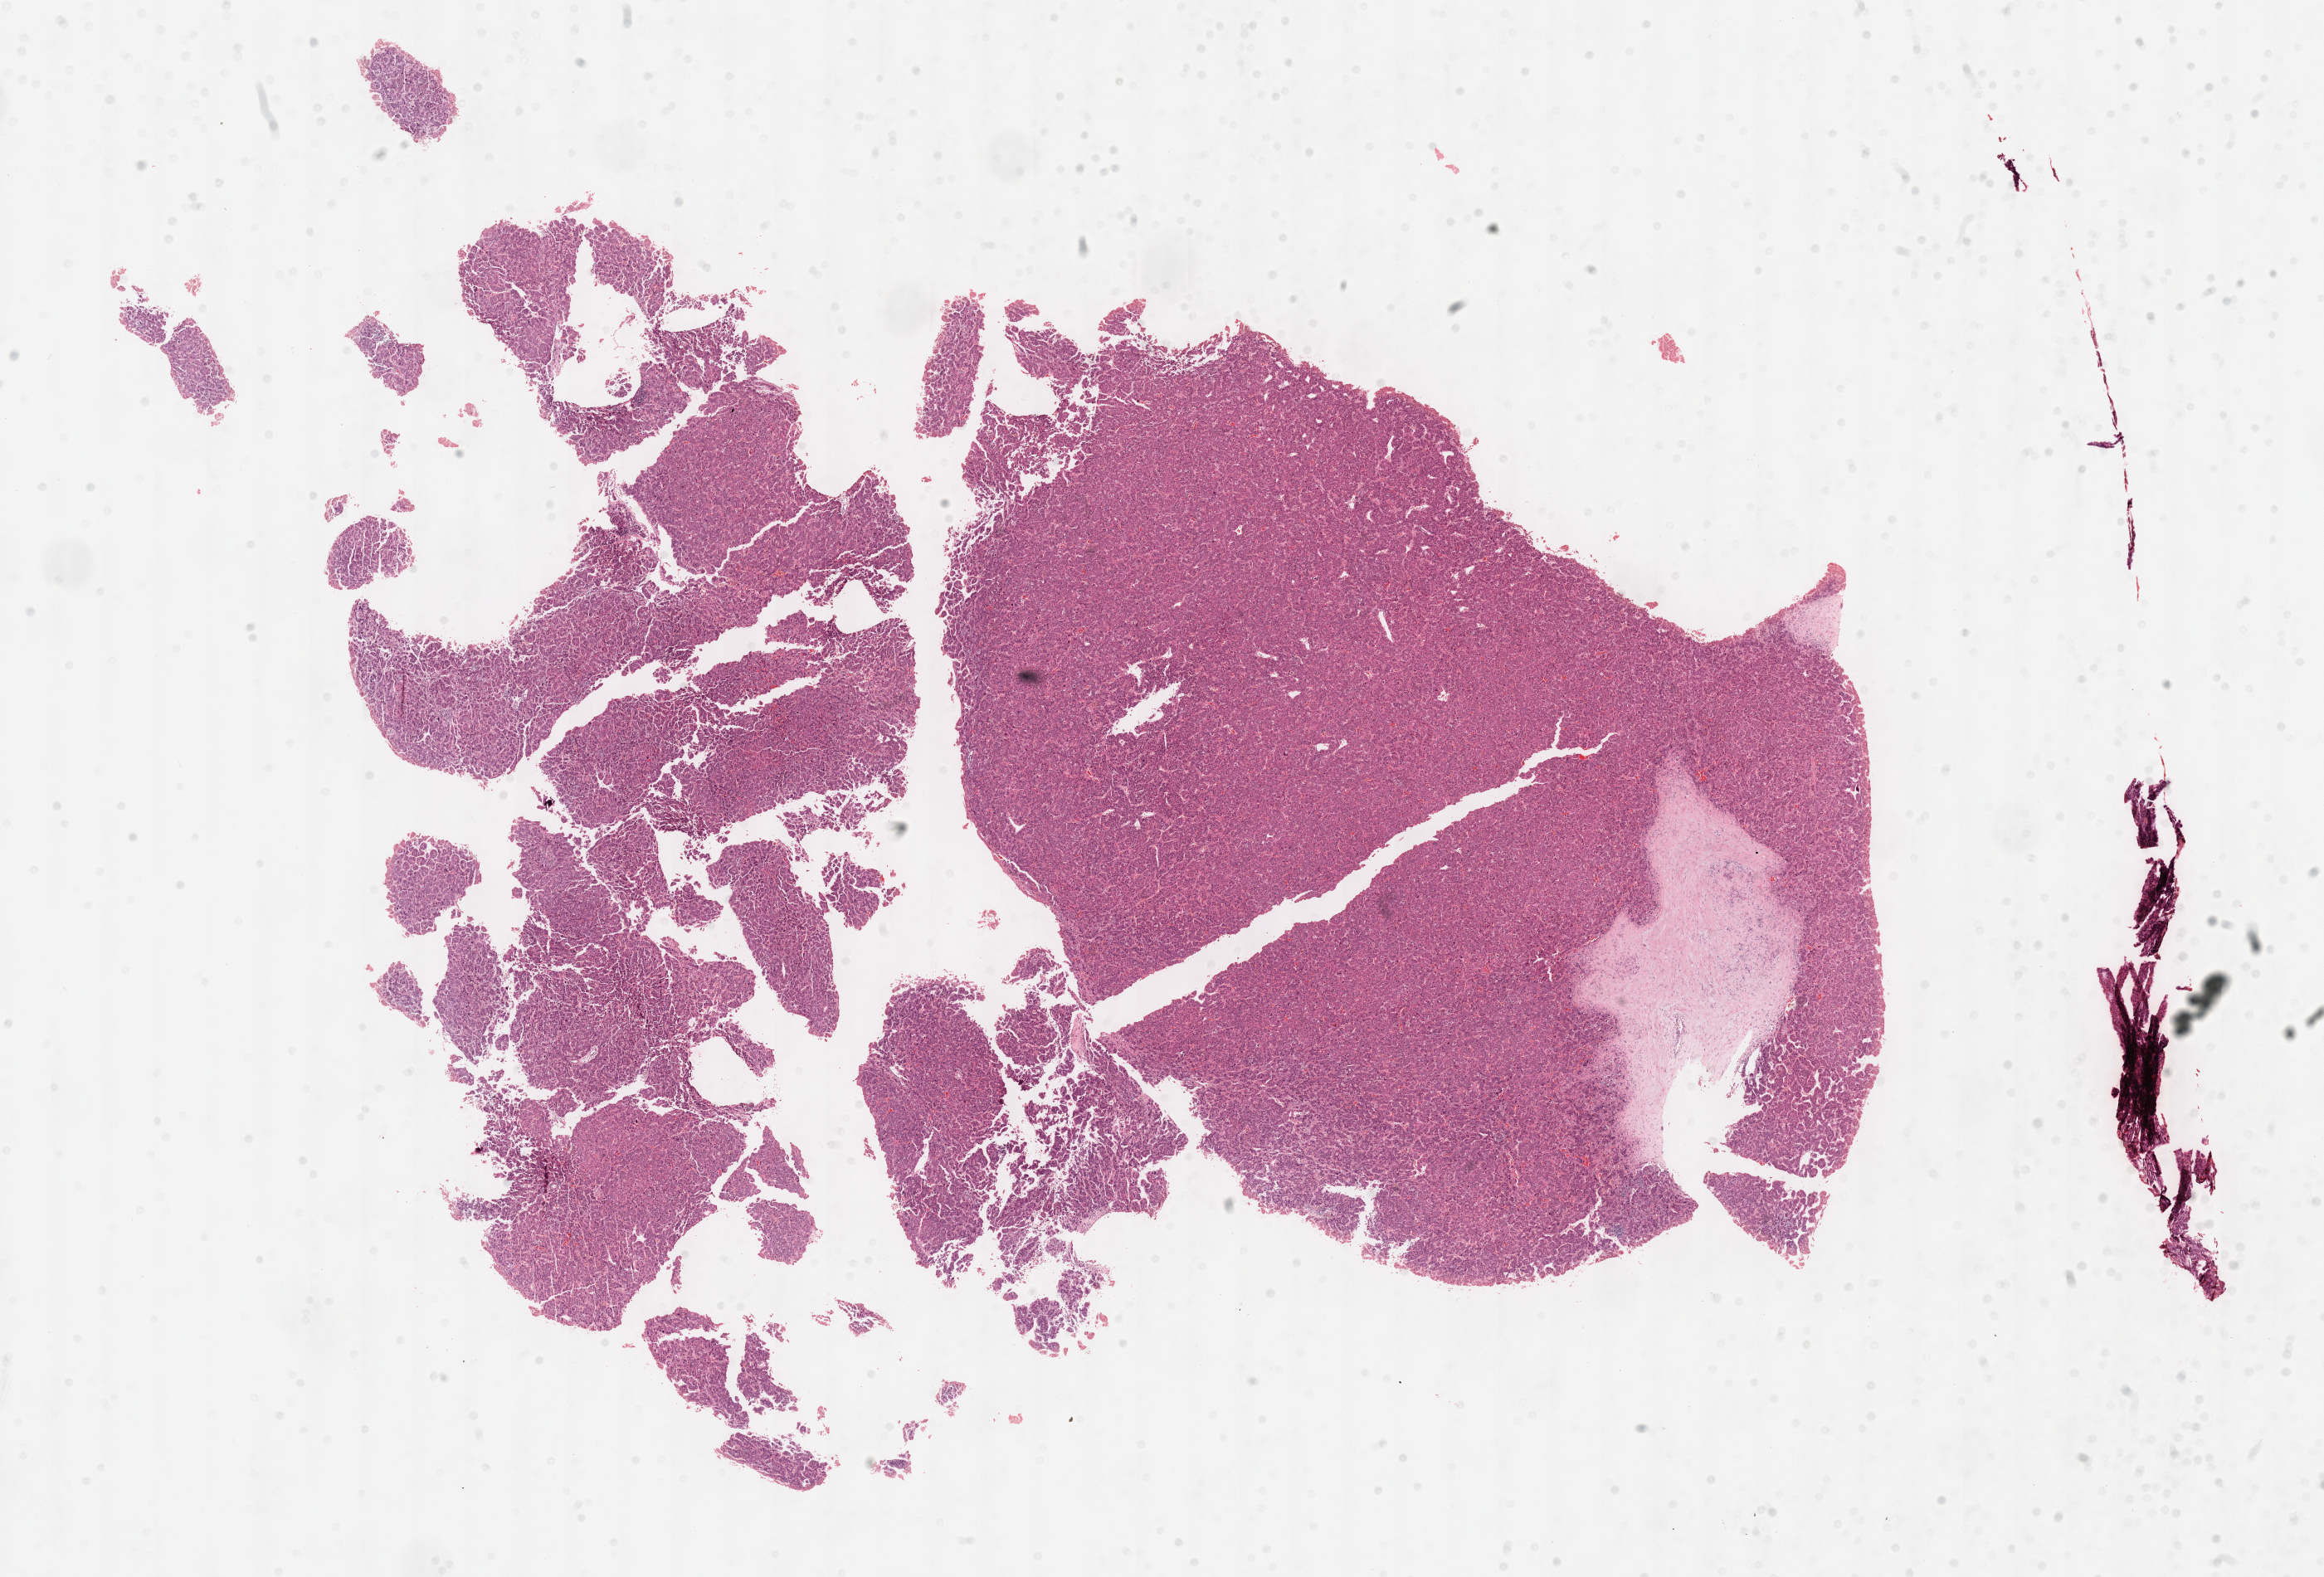
H&E whole-slide image, shown as a low-resolution overview of the whole scanned area (about 22.6 x 15.4 mm, from a 40x scan), FFPE section, primary tumour sample from the liver. Patient: male, age at initial diagnosis 52 years.
Histologic diagnosis: Hepatocellular carcinoma, NOS.